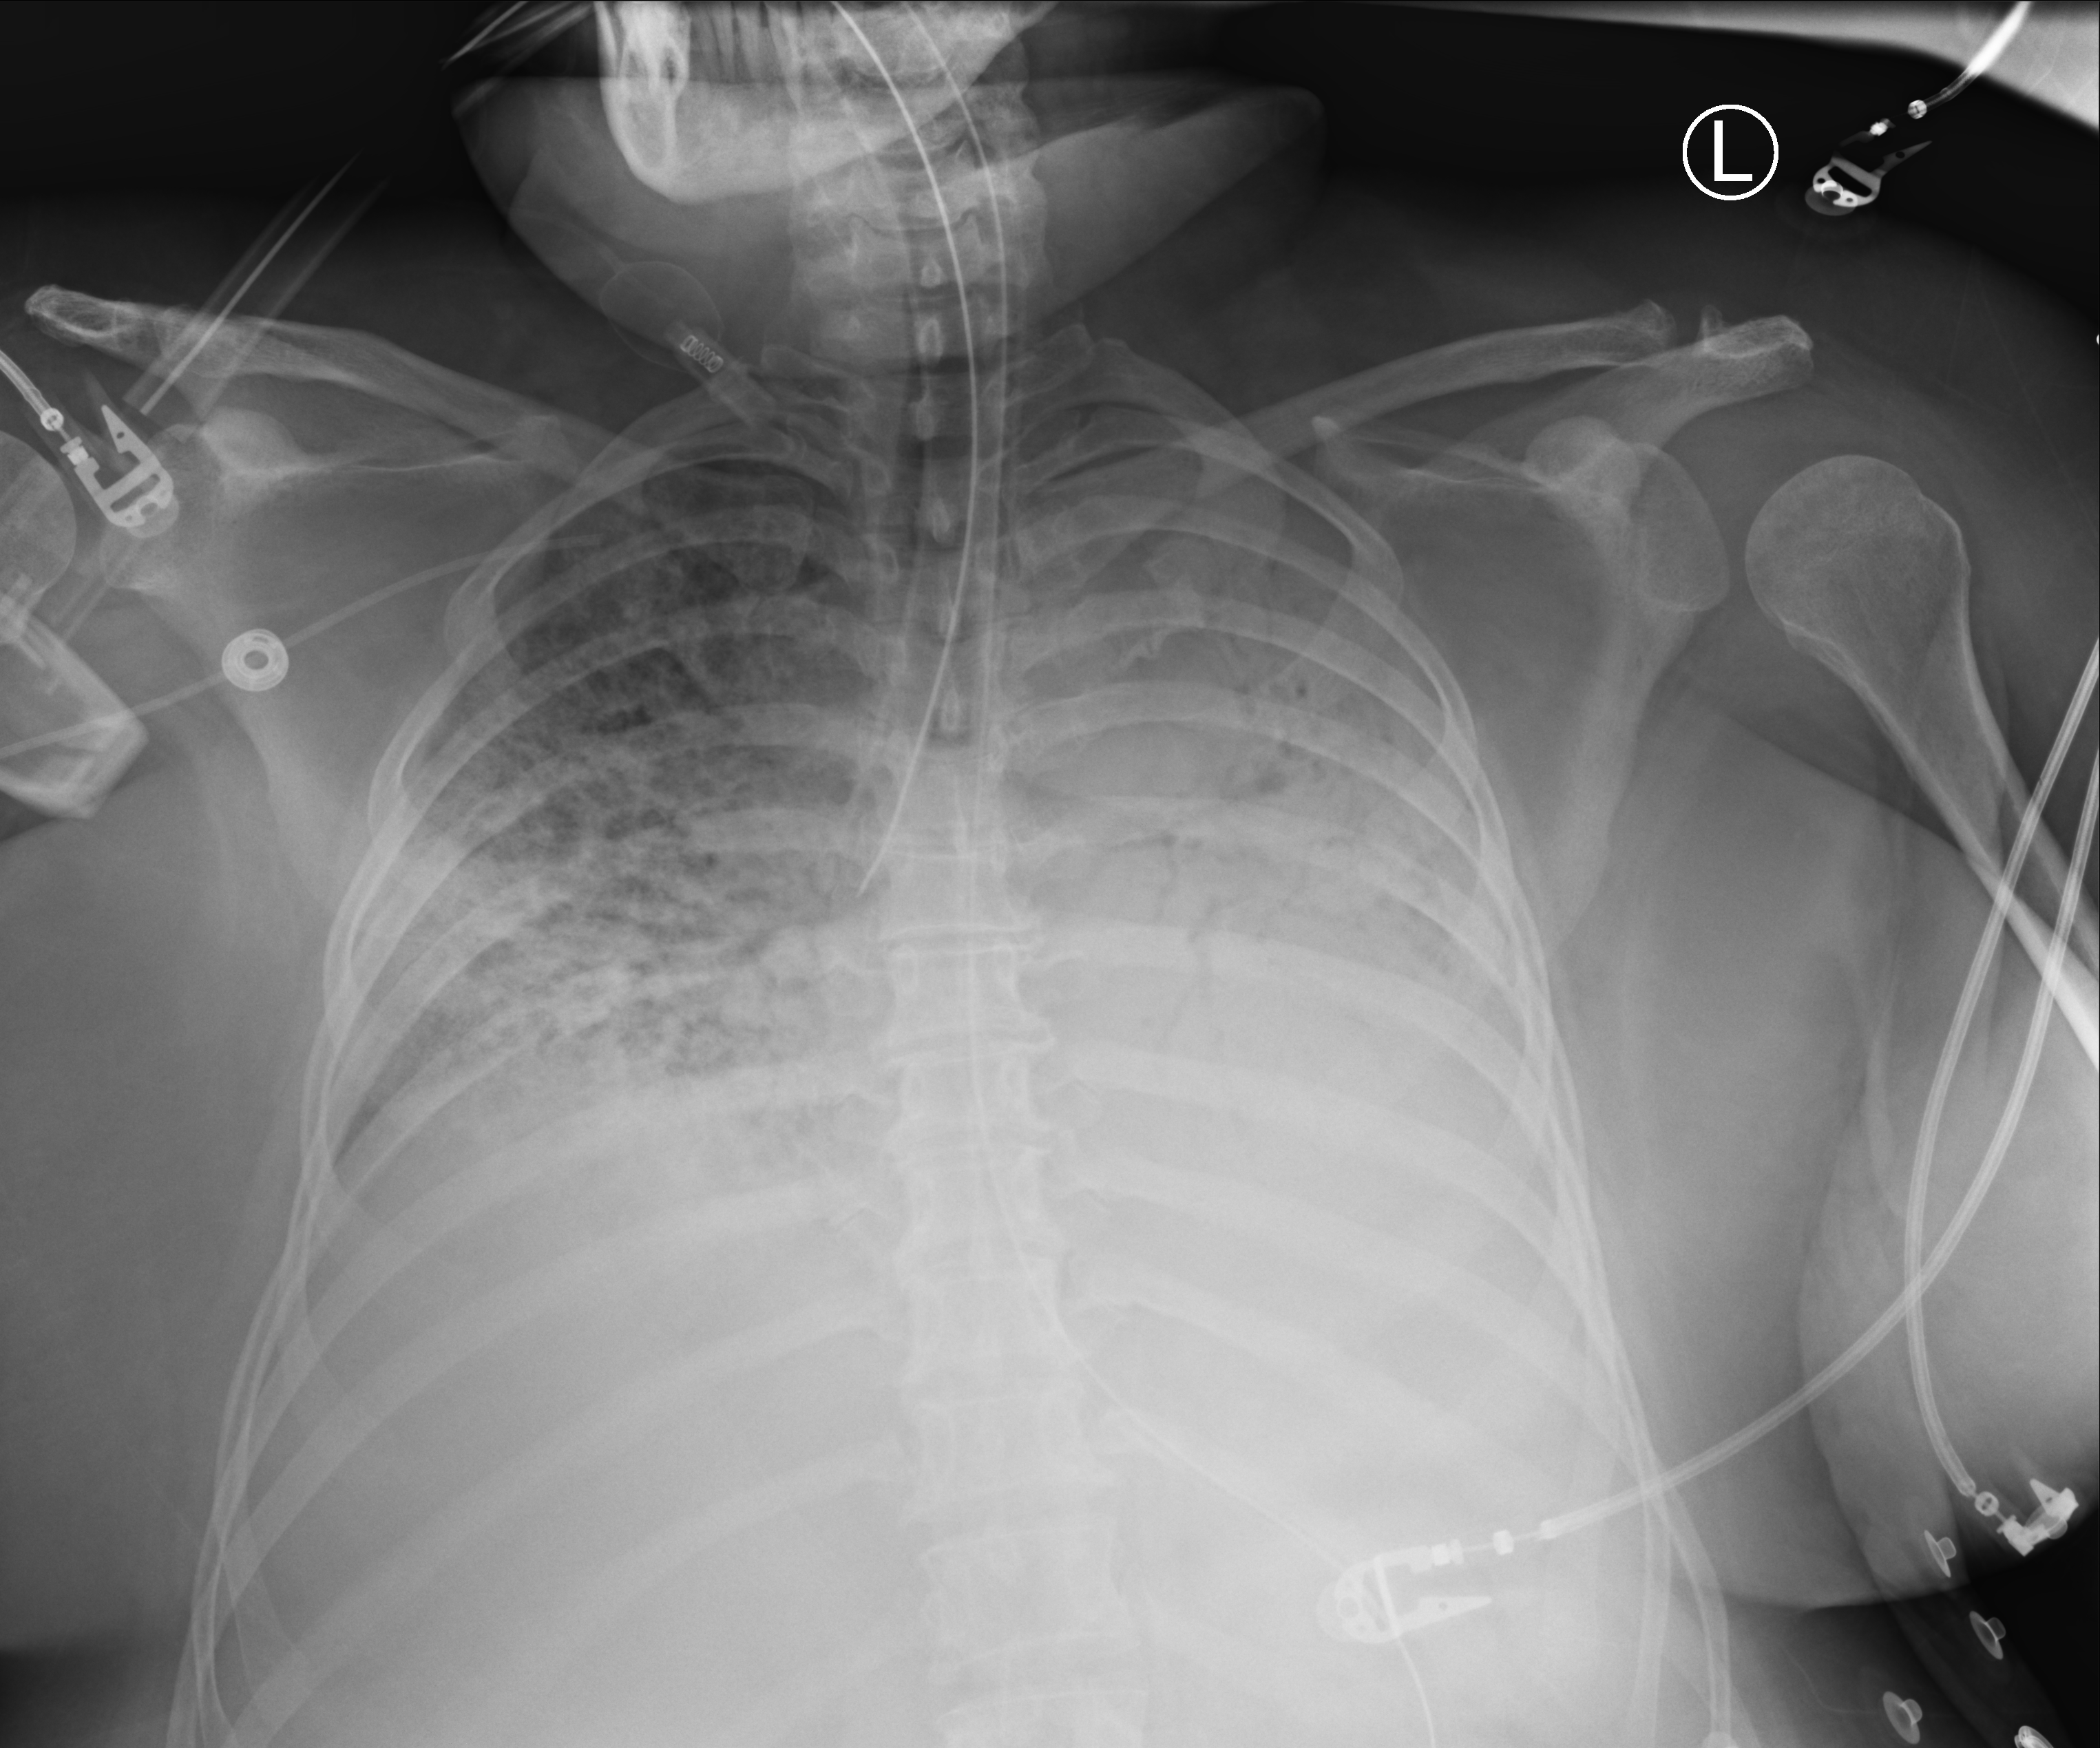
Bedside chest radiograph (computed radiography), anteroposterior (AP) projection. Patient hospitalised with COVID-19; female, aged 18–59 years.
Hospital-stay facts (about this admission, not read from this image; timing relative to this image not recorded): mechanically ventilated during this hospital stay: yes; admitted to intensive care during this hospital stay: yes.